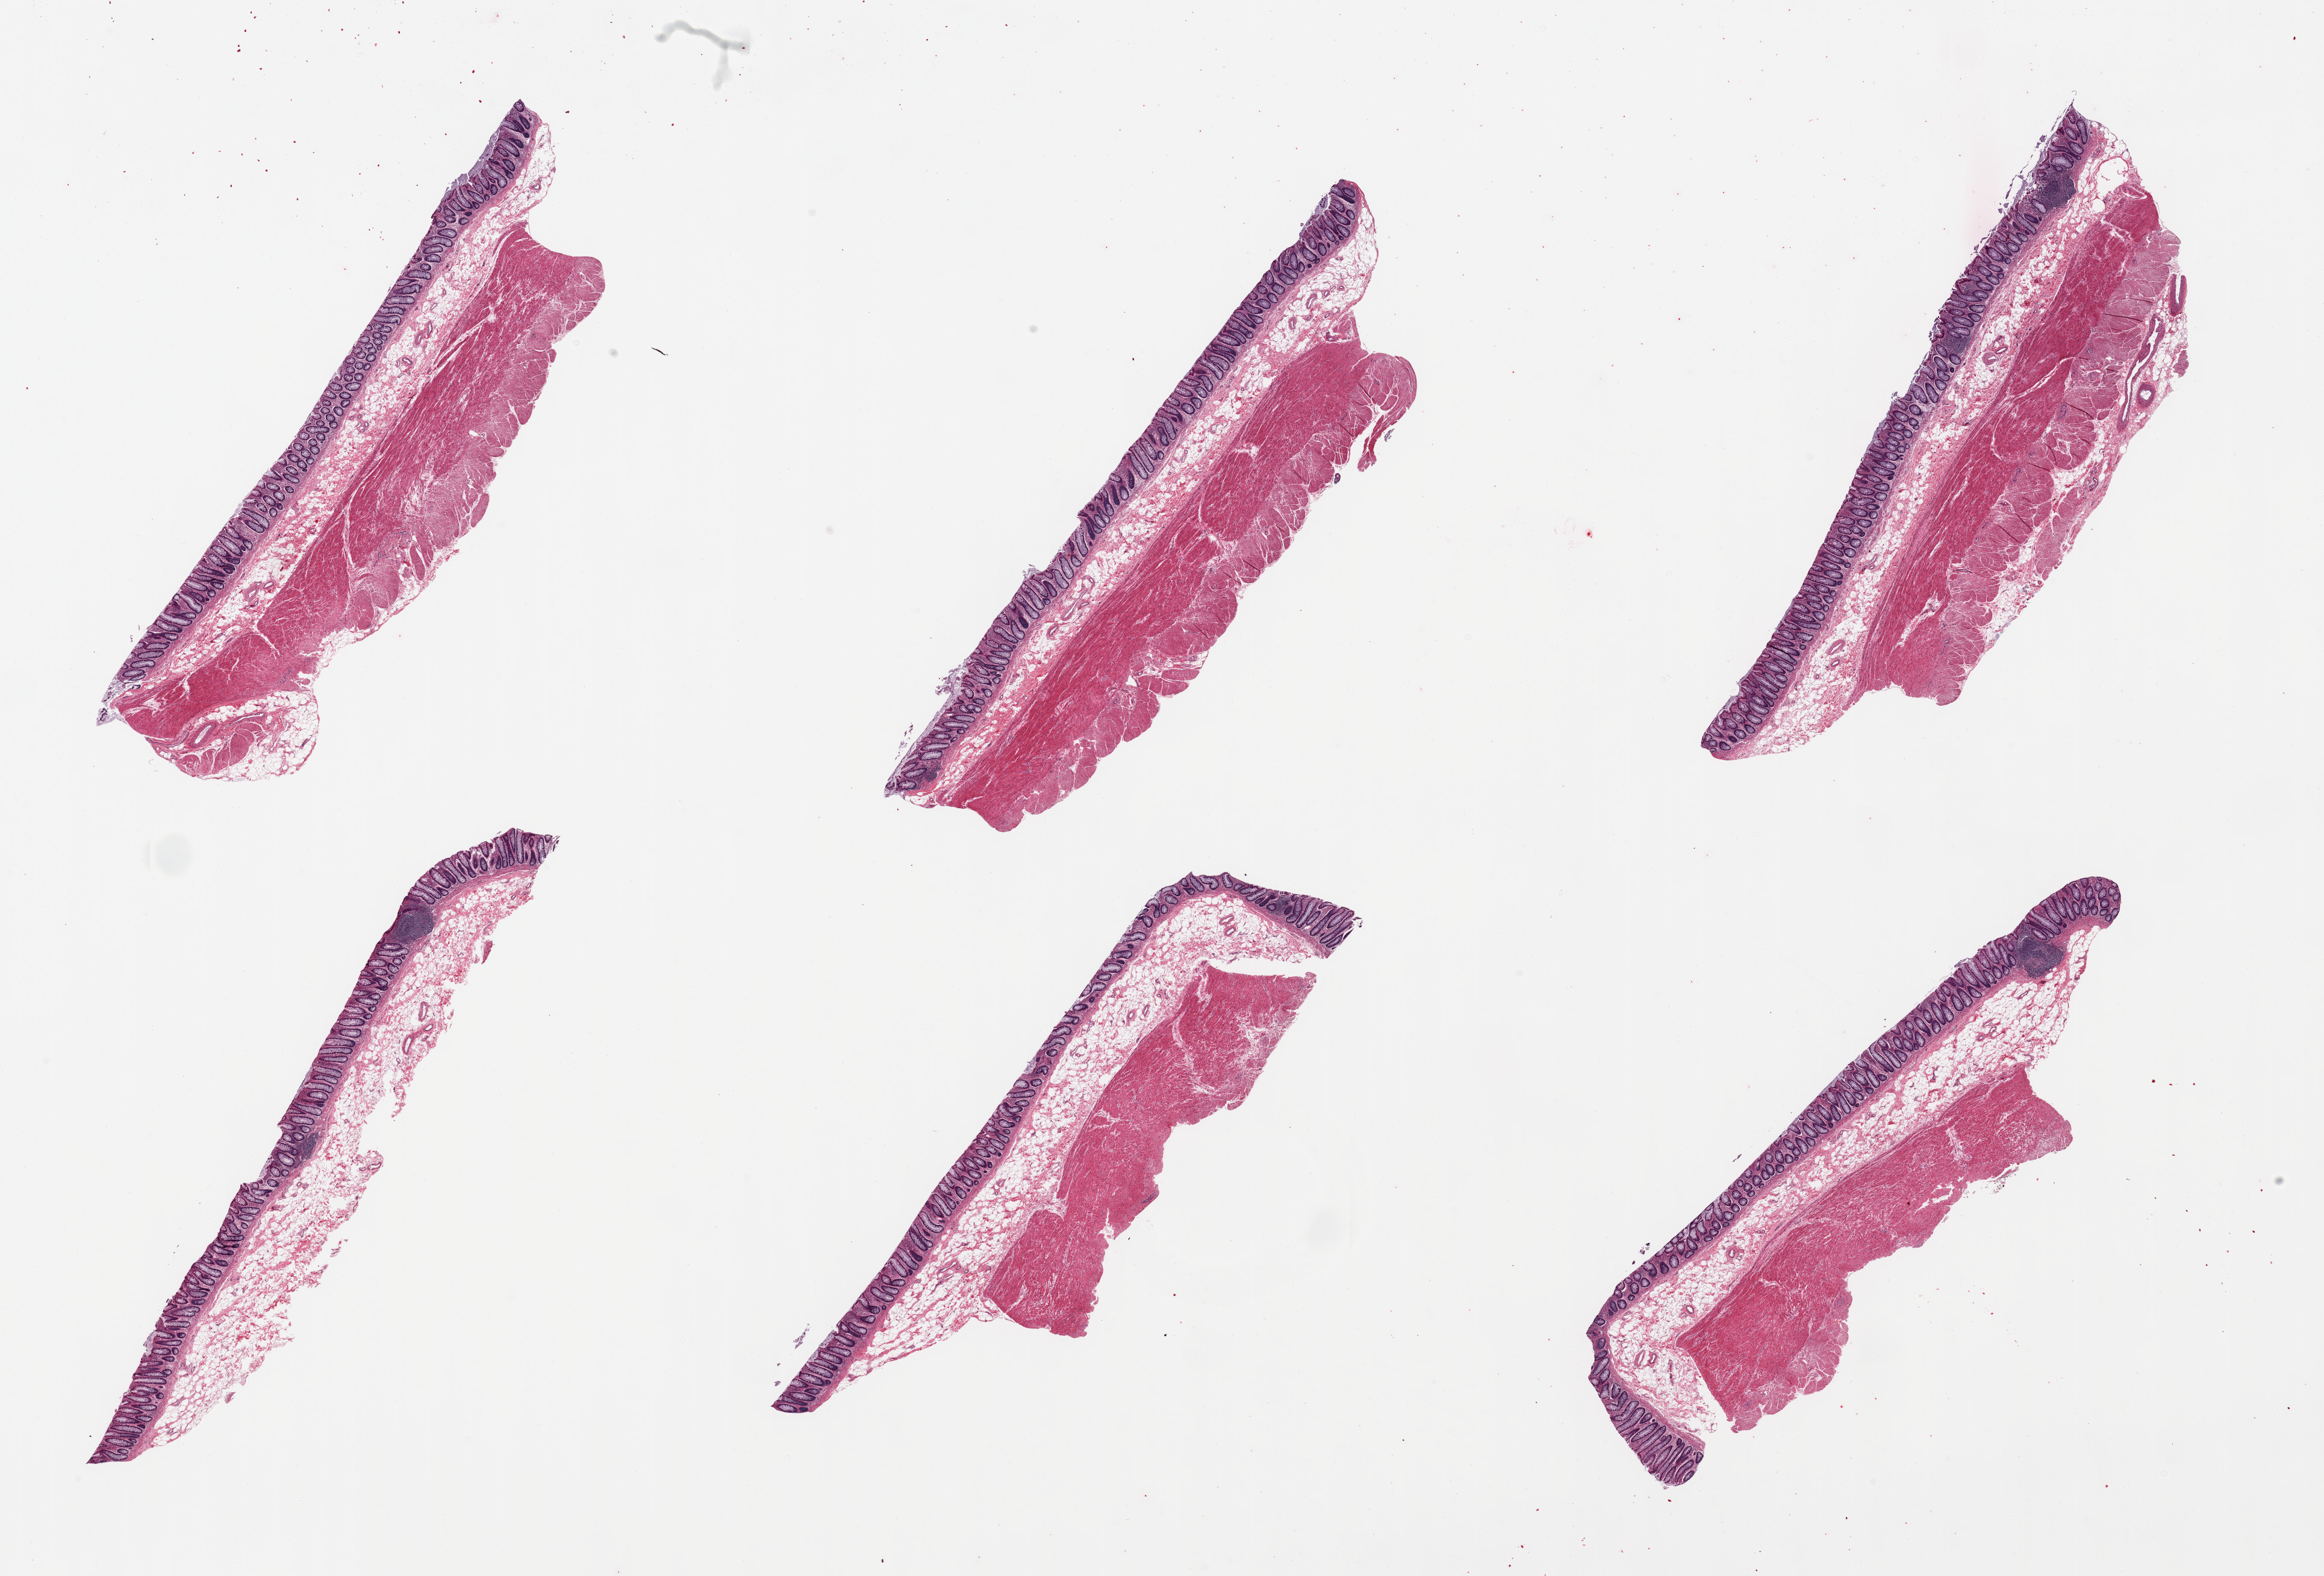
H&E whole-slide image — low-resolution overview of the scanned area, about 30.5 x 20.7 mm (acquisition: 20x scan), PAXgene-fixed, paraffin-embedded tissue, section of ileum (target tissue), donor tissue sample. Male donor.
Pathologist's review note for this sample: 6 pieces; mild to moderate autolysis, colon, not ileum.